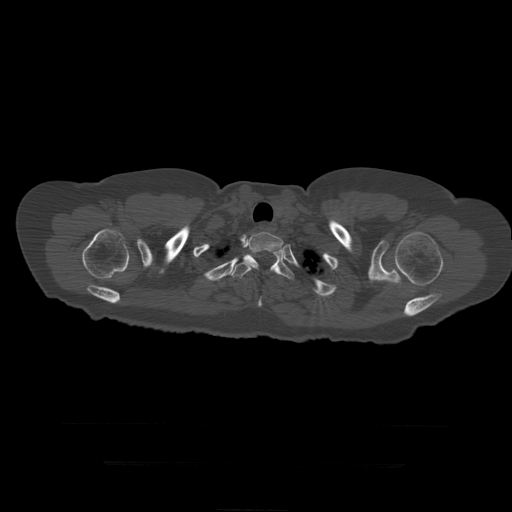
CT including the spine, one axial slice; slice 368 of 399 in the series (ordered by position); reconstruction kernel STANDARD; 120 kVp; bone window (W 1800 / L 400 HU); 512 × 512 image matrix. Patient age 41 years. Case-level facts recorded for this patient, not image findings: primary cancer: breast.
Structures marked on this image (semi-automatic segmentation, software-assisted and operator-edited):
- T2 vertebra: bounding box <246,232,285,273> (left, top, right, bottom; pixels)
- T3 vertebra: <229,250,295,307>